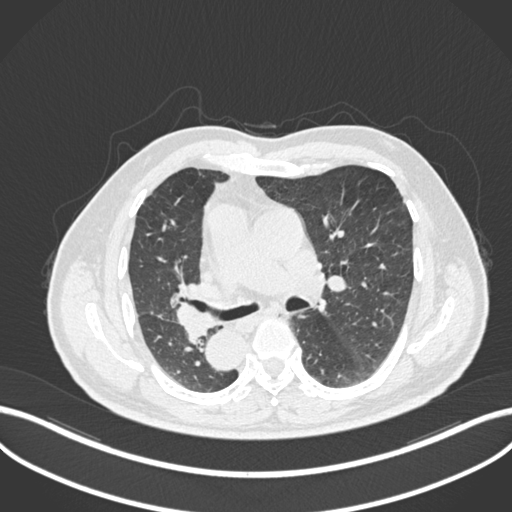
Chest CT, one axial slice. Position 130 of 206 along the scan axis. Lung window (W 1500 / L -600 HU). 1 mm slice thickness. 512 × 512 image matrix. Patient: male, 67 years. Case-level facts recorded for this patient, not image findings: clinical TNM (as recorded): T2a N0 M0.
Annotated regions visible in this slice (rectangle marked by the reading radiologist):
- lung tumour (recorded histology: squamous cell carcinoma): bounding box <171,280,219,339> (left, top, right, bottom; pixels)